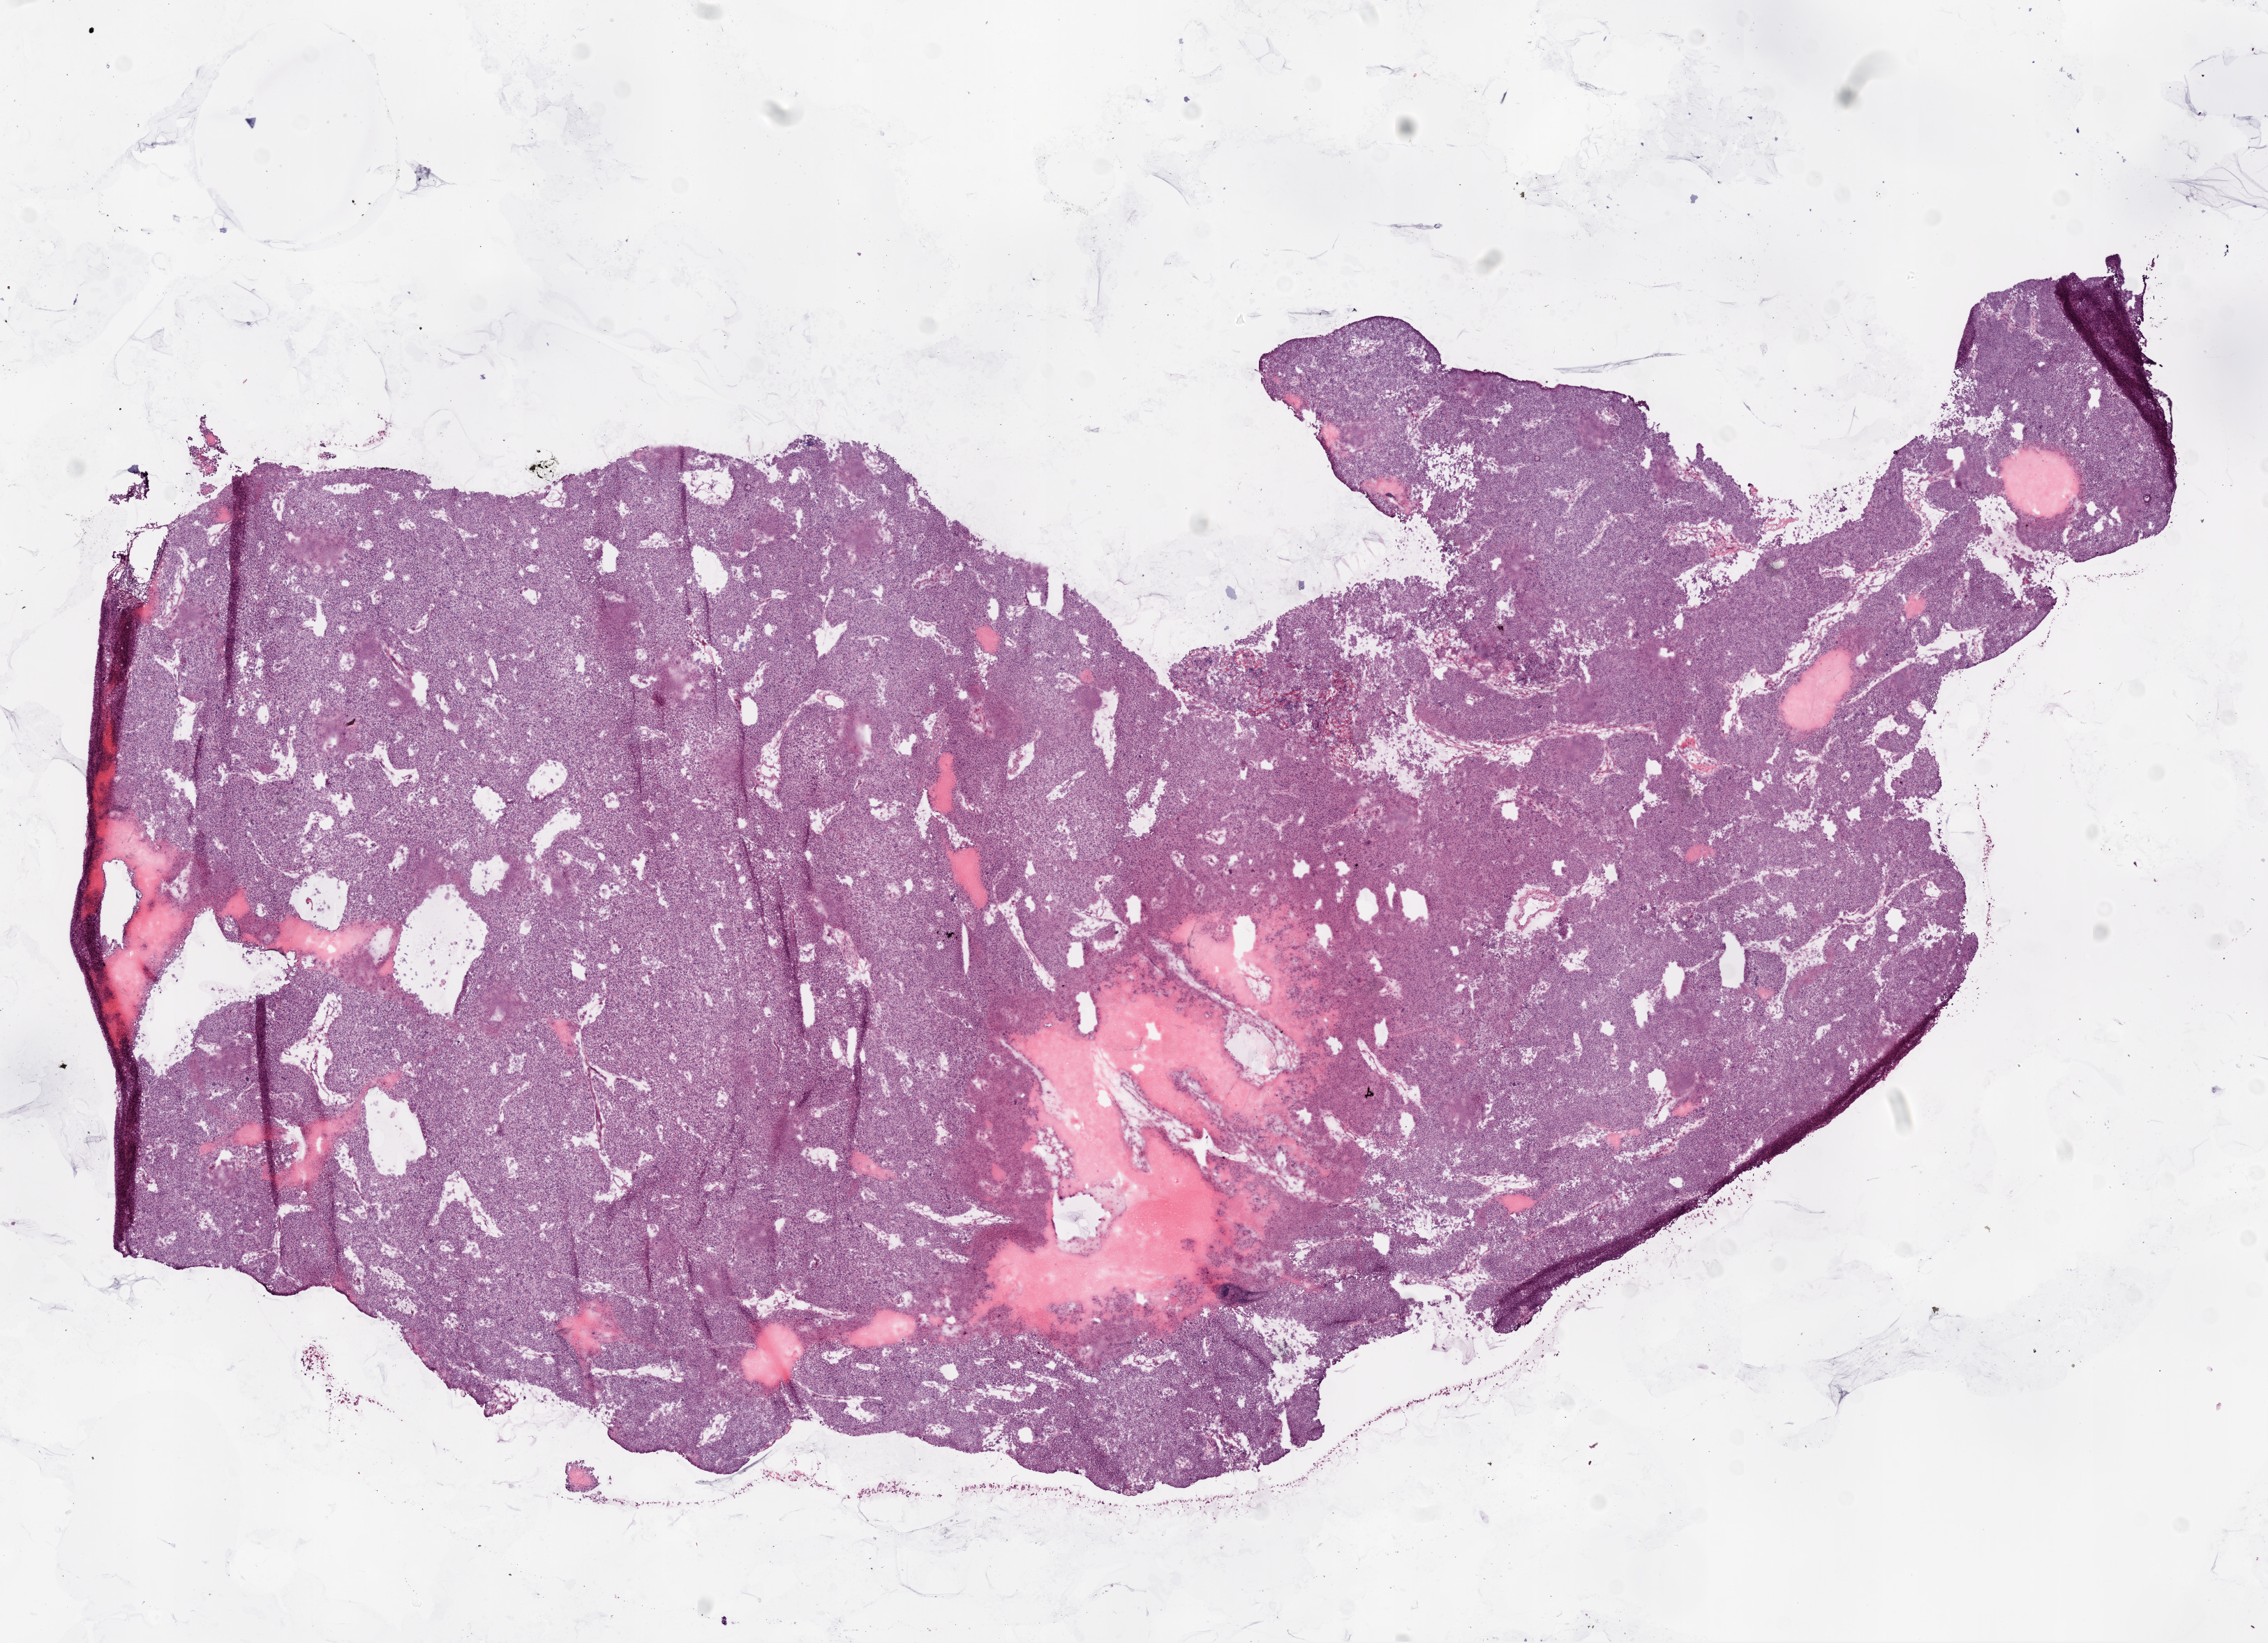
Whole-slide histology image, H&E-stained — whole scanned area (about 13.0 x 9.4 mm, acquisition: 20x scan) shown as a low-resolution overview; frozen section from the top of the tissue portion; primary tumour sample from the ovary. Female patient; age at initial diagnosis 49 years. Histologic grade: G3 (poorly differentiated). Composition of this section per pathologist review: tumour cells 94%, tumour nuclei 95%, normal cells 0%, stromal cells 5%, necrosis 1%.
Pathologic diagnosis: Serous cystadenocarcinoma, NOS. FIGO stage: IC.